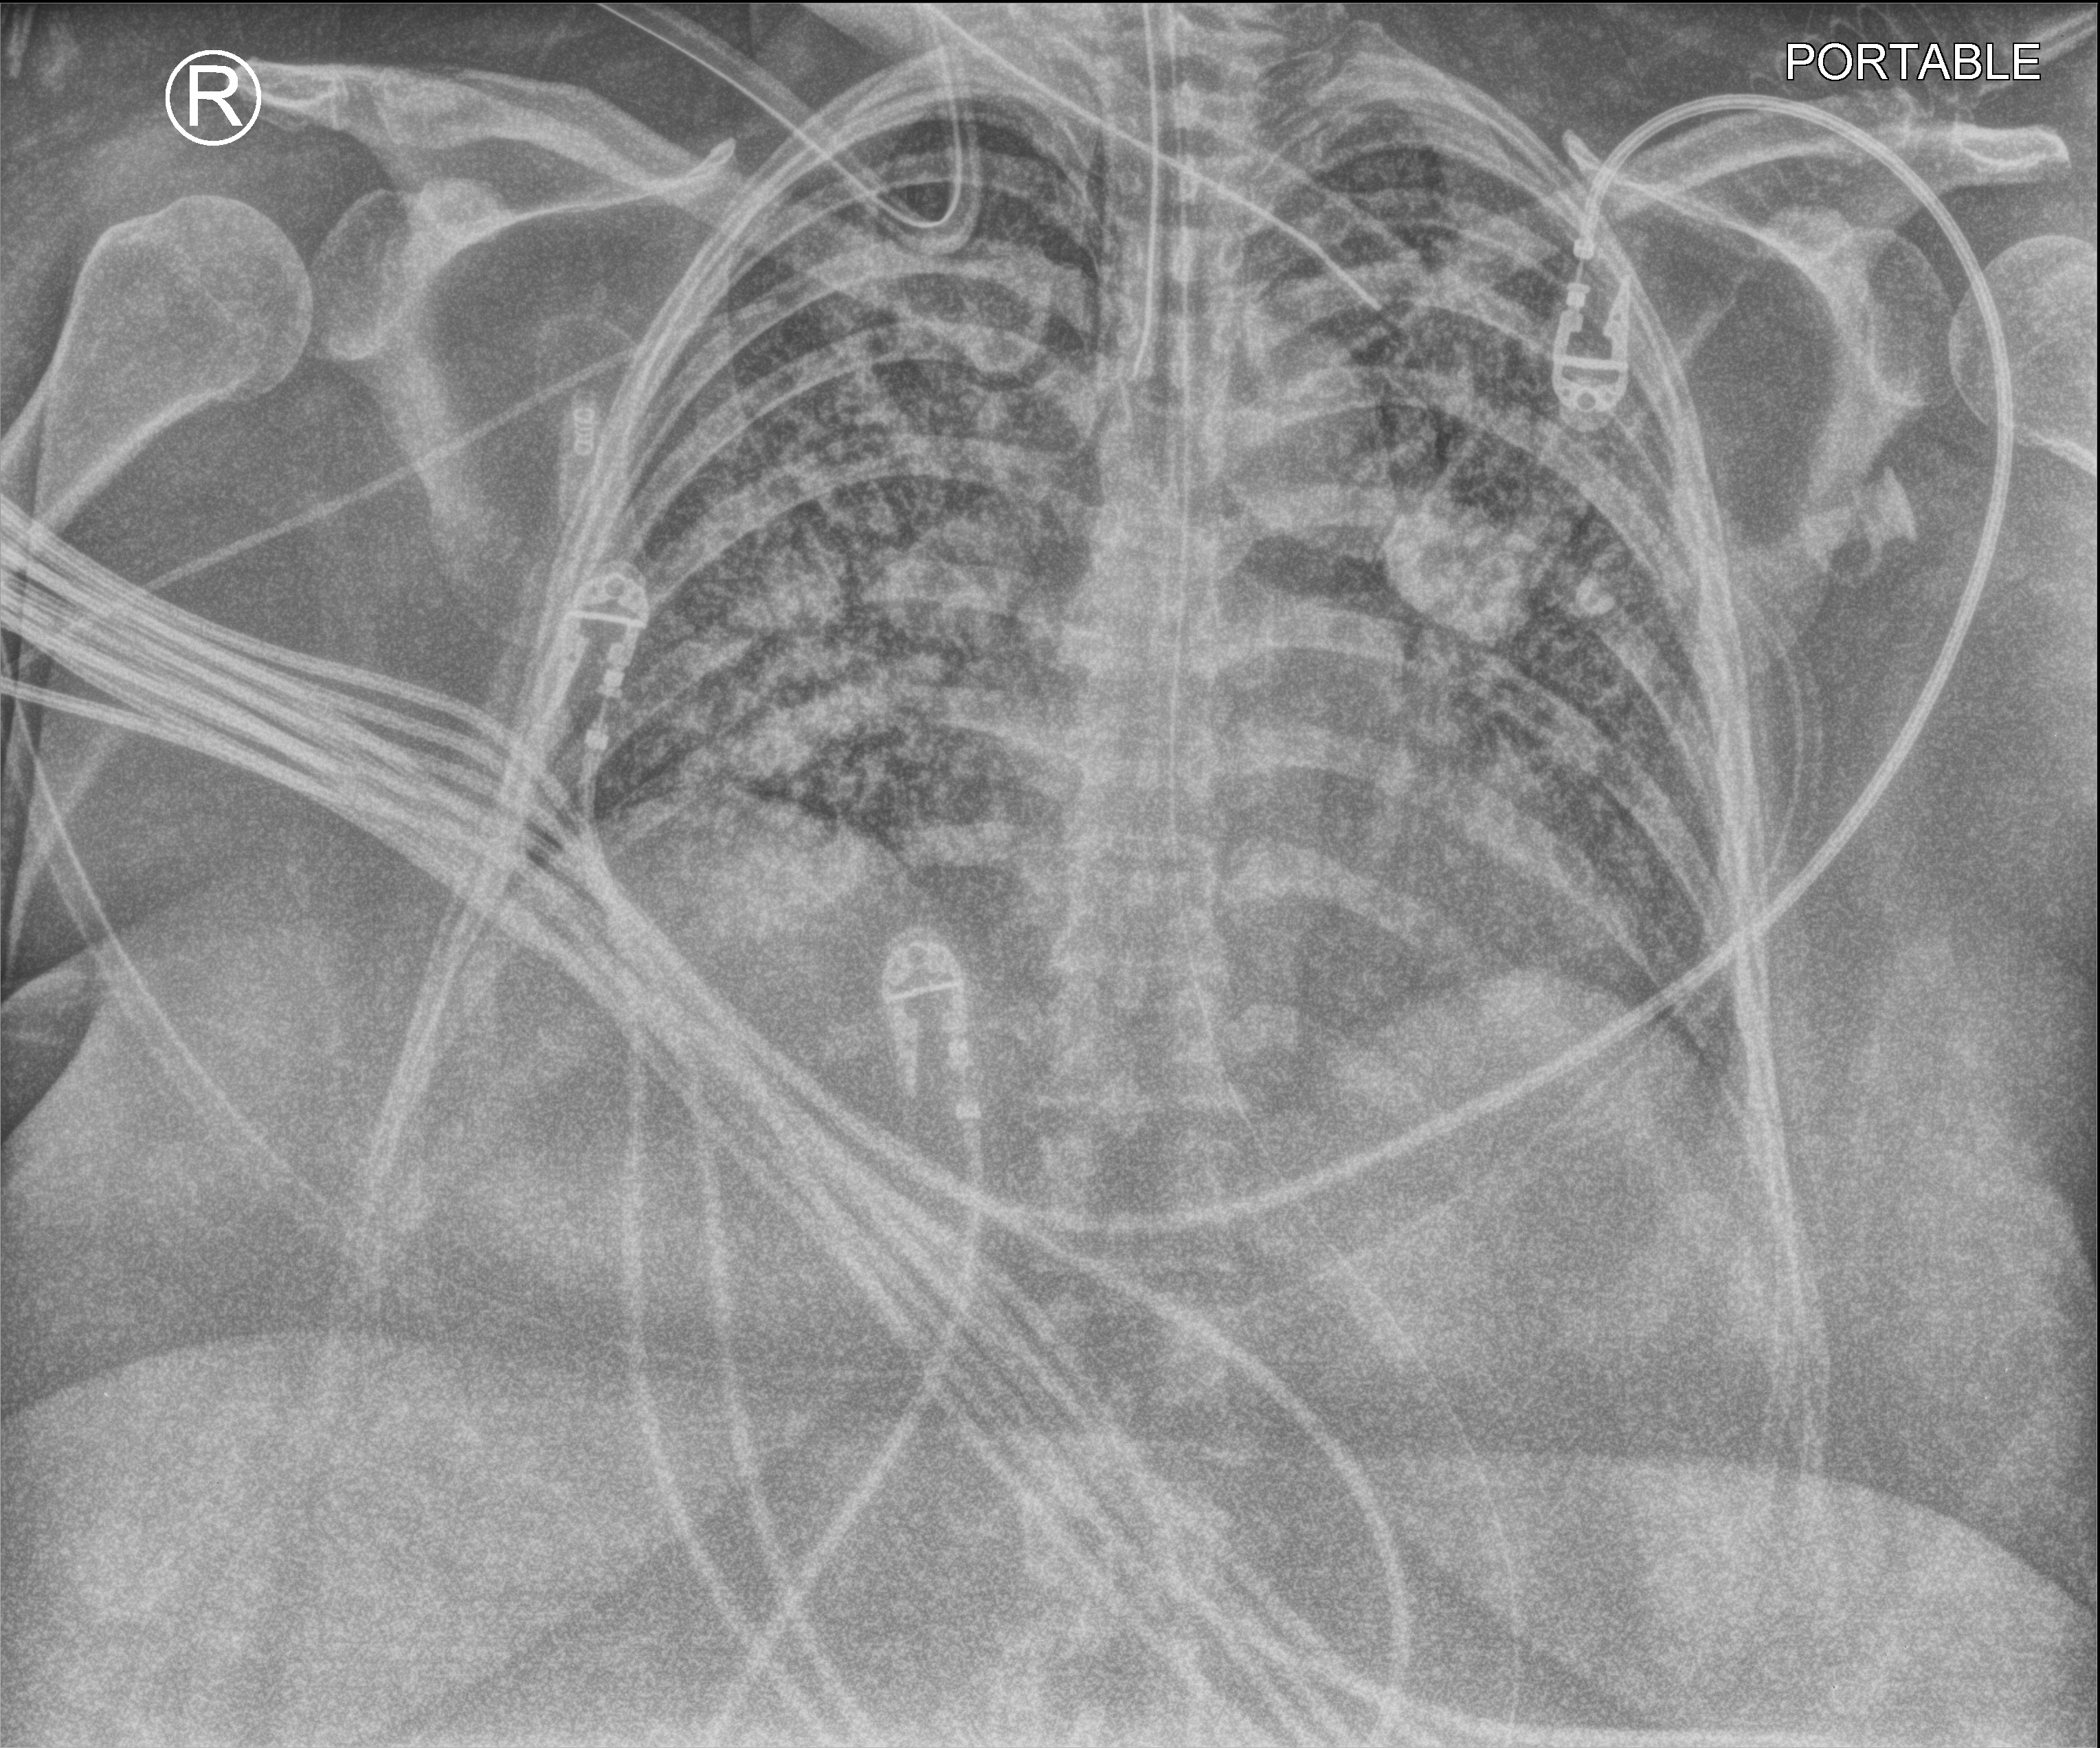
Bedside chest radiograph (computed radiography). Patient hospitalised with COVID-19; female, aged 18–59 years.
Hospital-stay facts (about this admission, not read from this image; timing relative to this image not recorded):
- admitted to intensive care during this hospital stay: yes